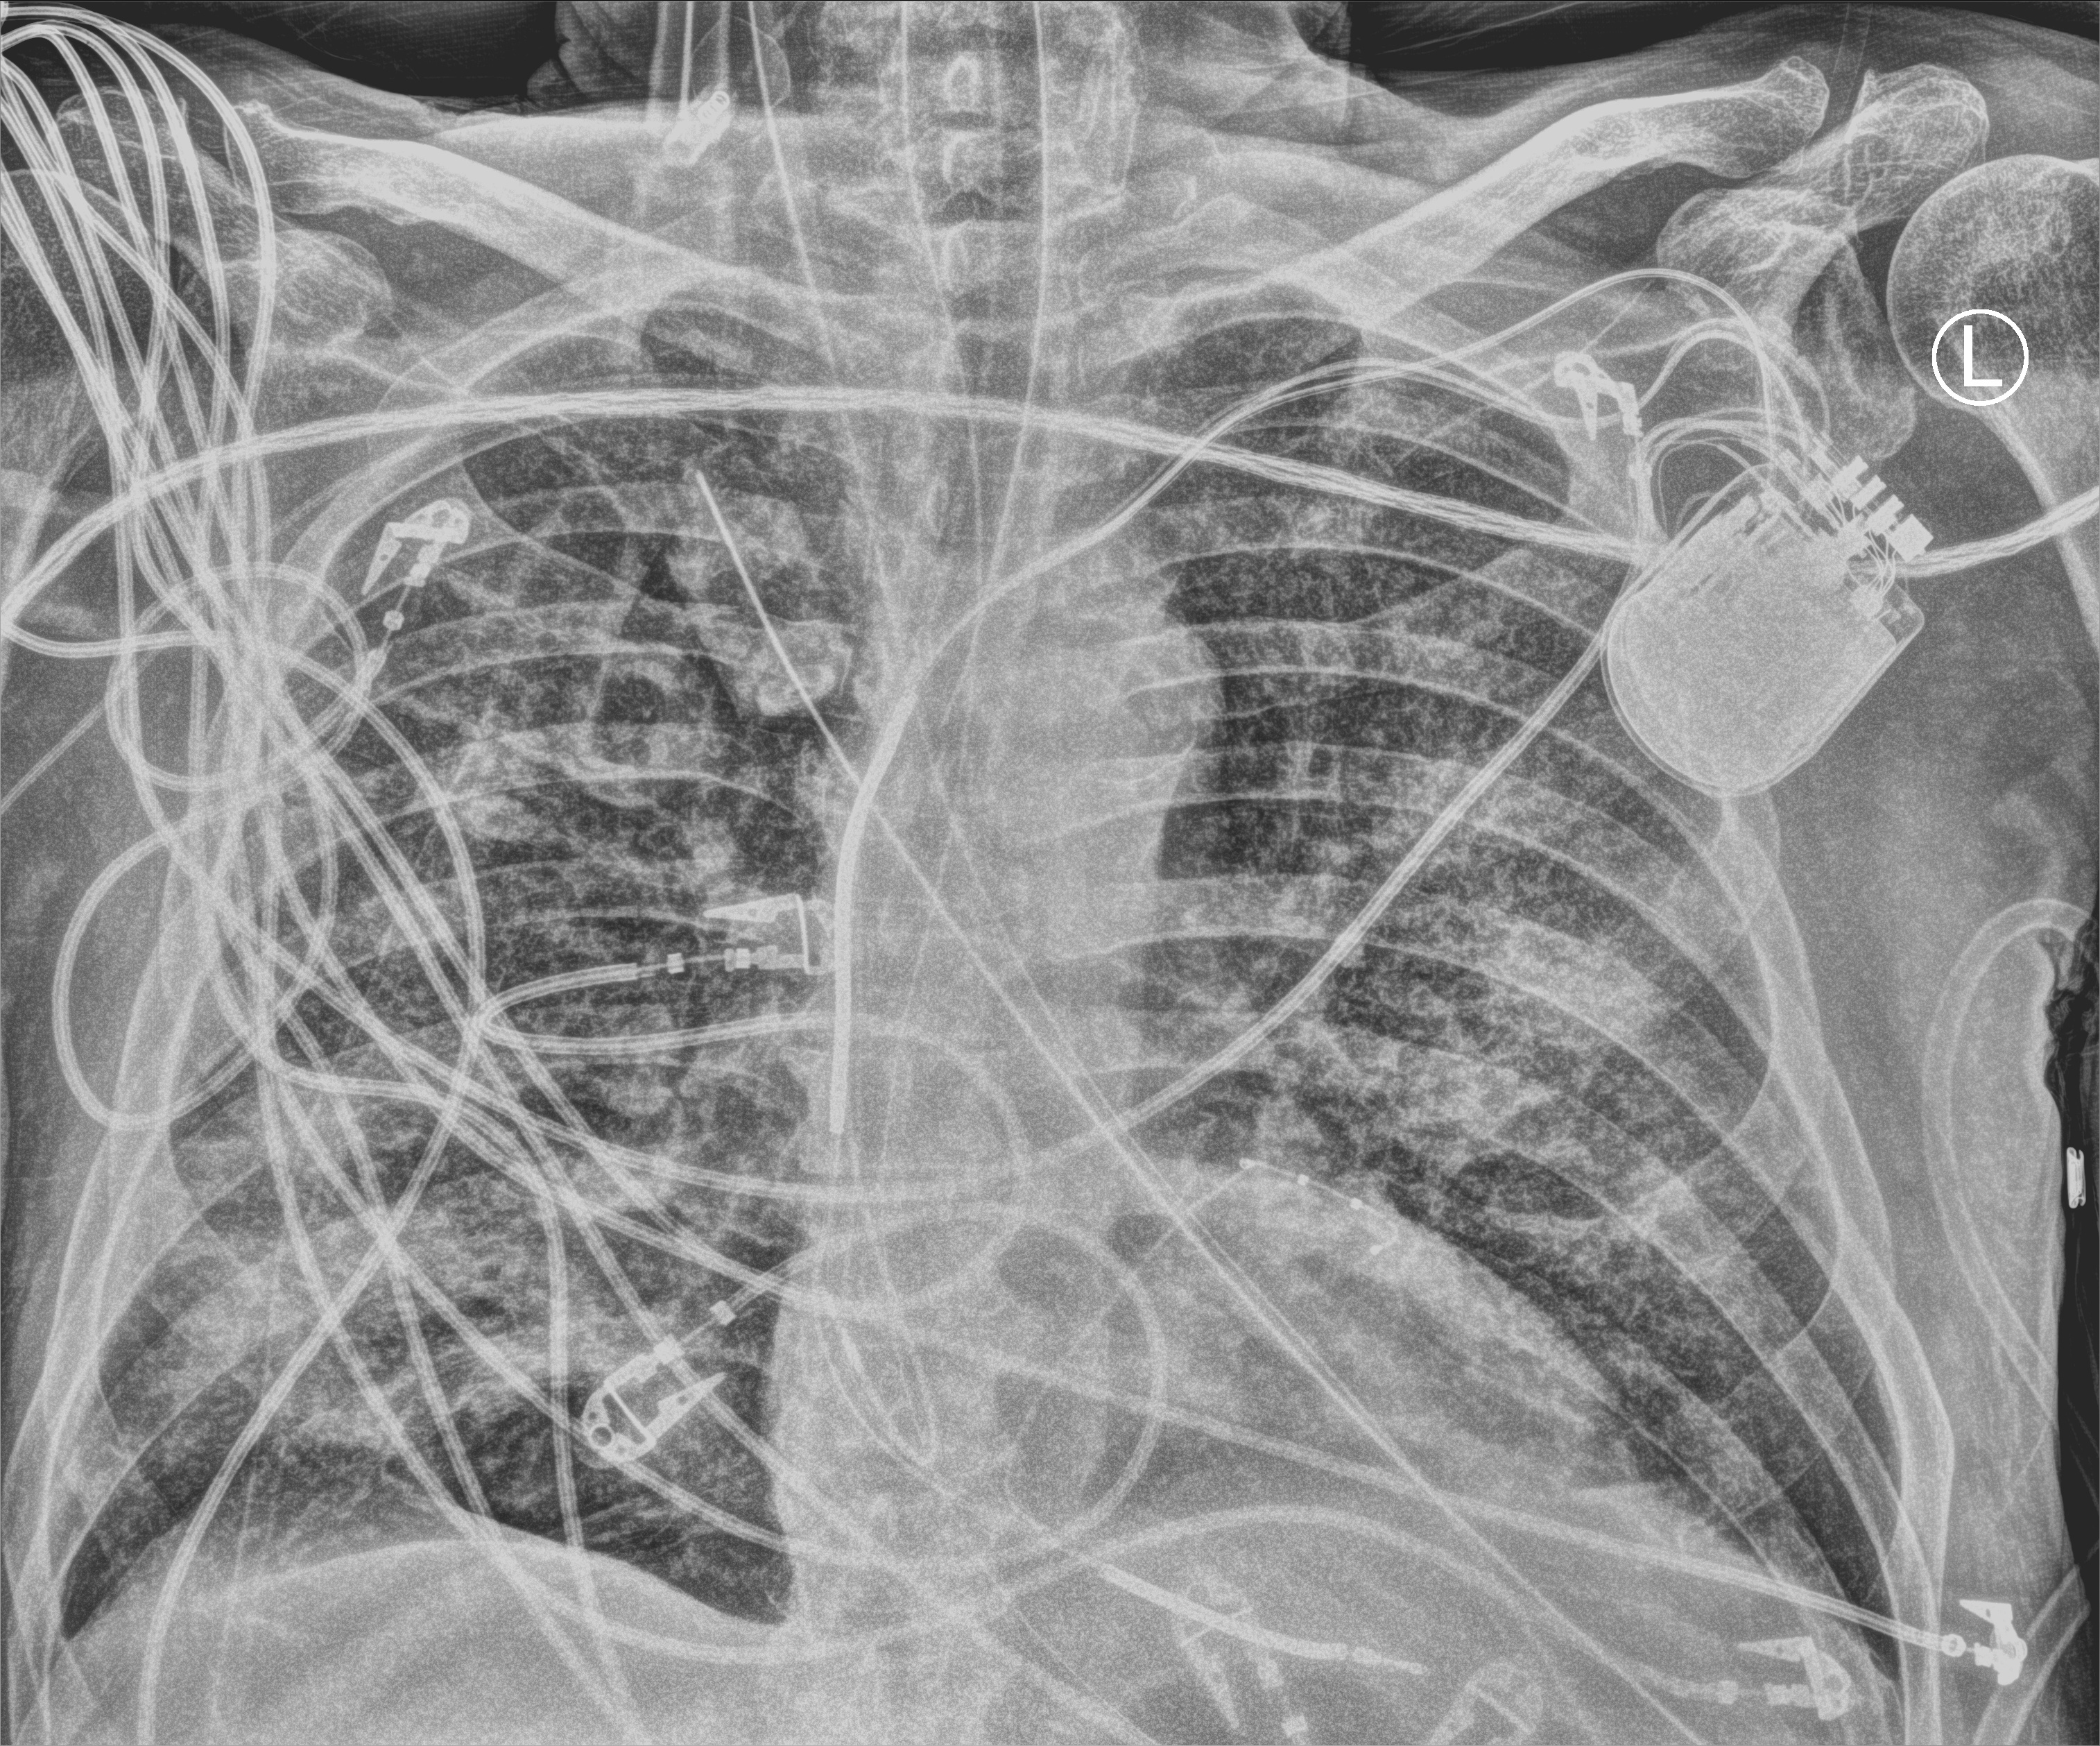
Bedside chest radiograph (computed radiography); anteroposterior (AP) projection. Male patient hospitalised with COVID-19, age 60–74 years.
Admission-level facts for this patient (not findings on this image; timing relative to this image not recorded):
- chronic kidney disease (admission record): no
- mechanically ventilated during this hospital stay: yes
- admitted to intensive care during this hospital stay: yes